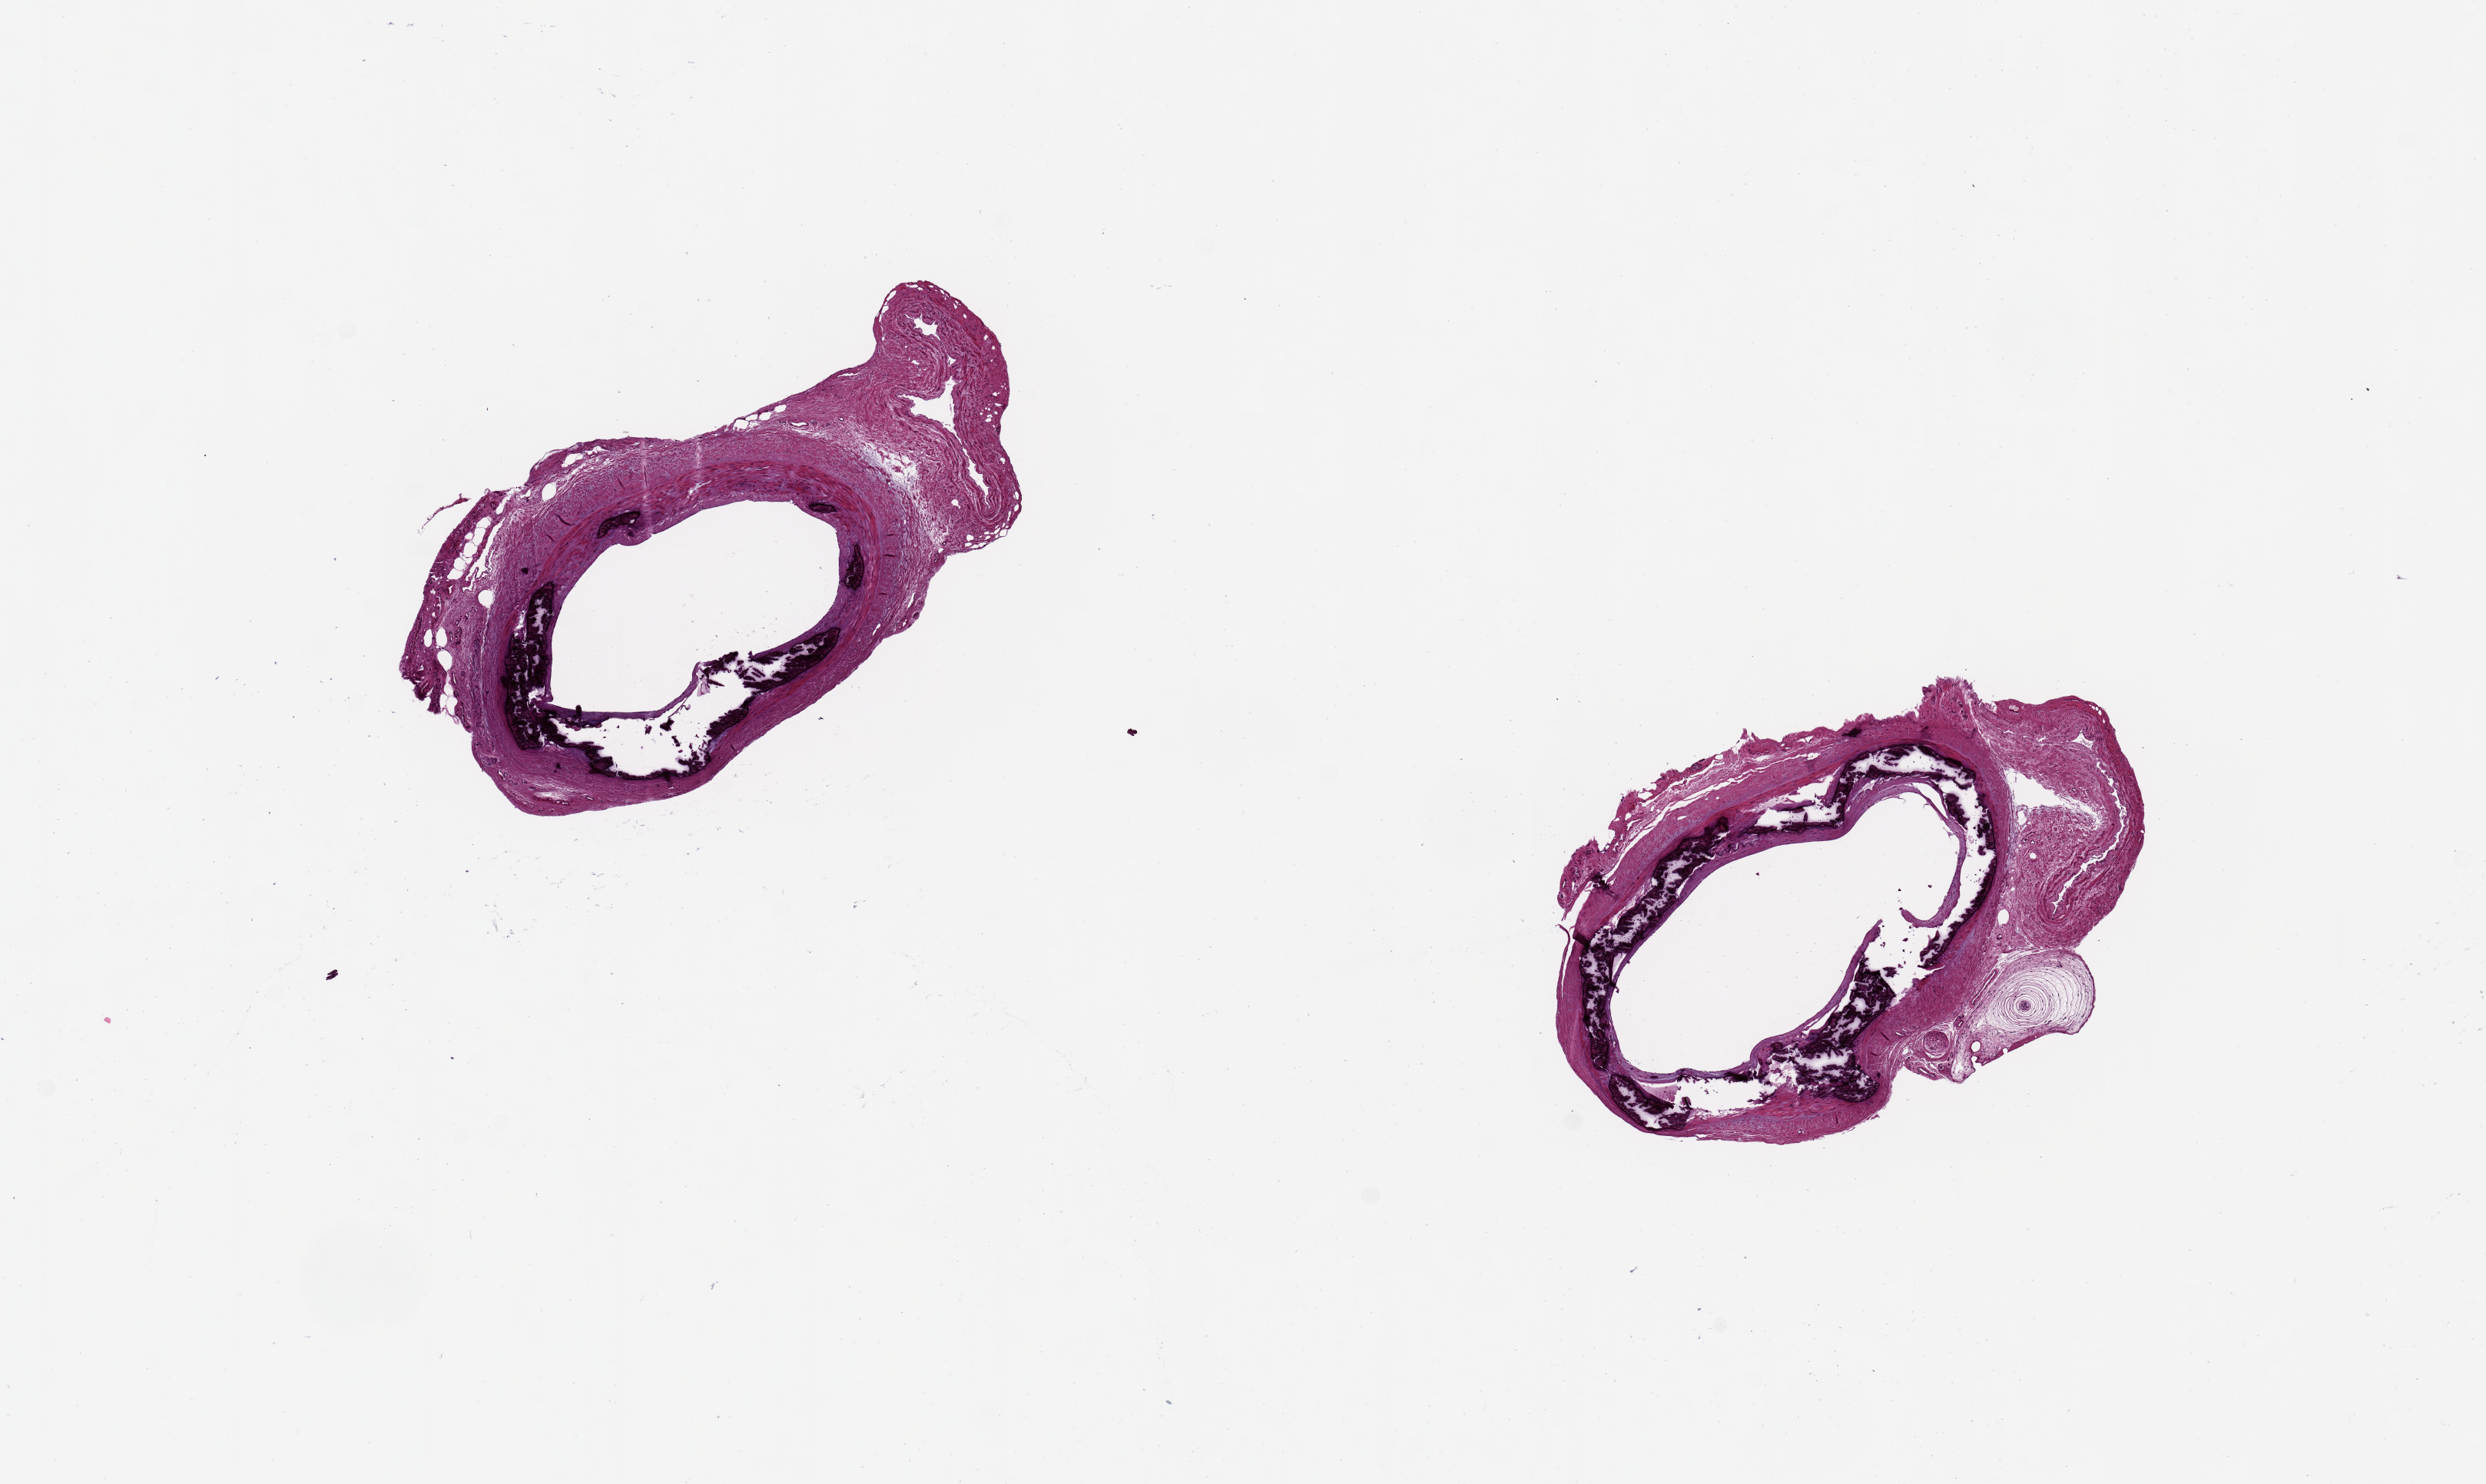
Whole-slide image, haematoxylin and eosin stain, low-resolution overview of the scanned area, about 12.8 x 7.6 mm, PAXgene-fixed, paraffin-embedded tissue, sampled site (target tissue): tibial artery, donor tissue sample. Donor sex: female.
* pathologist's review note for this sample: 2 calcified arteries, ~2.5 mm diameter; 1 with adjacent nerve; both with adjacent vein